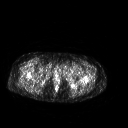
FDG PET of an extremity soft-tissue mass (from a PET/CT study), one axial slice. Position 257 of 267 along the scan axis. 3.27 mm slice thickness. 128 × 128 image matrix, field of view 500 × 500 mm. Patient: female, 42 years. Case-level facts recorded for this patient, not image findings: histological type: pleiomorphic leiomyosarcoma; grade: intermediate; site of the primary tumour: left thigh.
Annotated regions visible in this slice (expert contour drawn on MRI and transferred to this co-registered scan by the dataset authors):
- gross tumour volume including surrounding oedema: bounding box [x1, y1, x2, y2] px = [61, 65, 78, 75]
- gross tumour volume (mass): [70, 66, 77, 71]